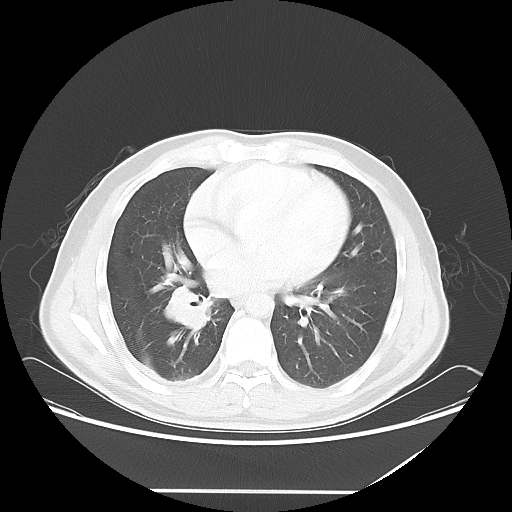
Chest CT, one axial slice; position 27 of 60 along the scan axis; reconstruction kernel LUNG; lung window (W 1500 / L -600 HU); 5 mm slice thickness; 512 × 512 image matrix. Patient: male, 48 years. From the clinical record (not read from this slice): clinical TNM (as recorded): T3 N3 M1a.
Annotated regions visible in this slice (rectangle marked by the reading radiologist):
- lung tumour (recorded histology: squamous cell carcinoma): bounding box <163,285,213,334> (left, top, right, bottom; pixels)